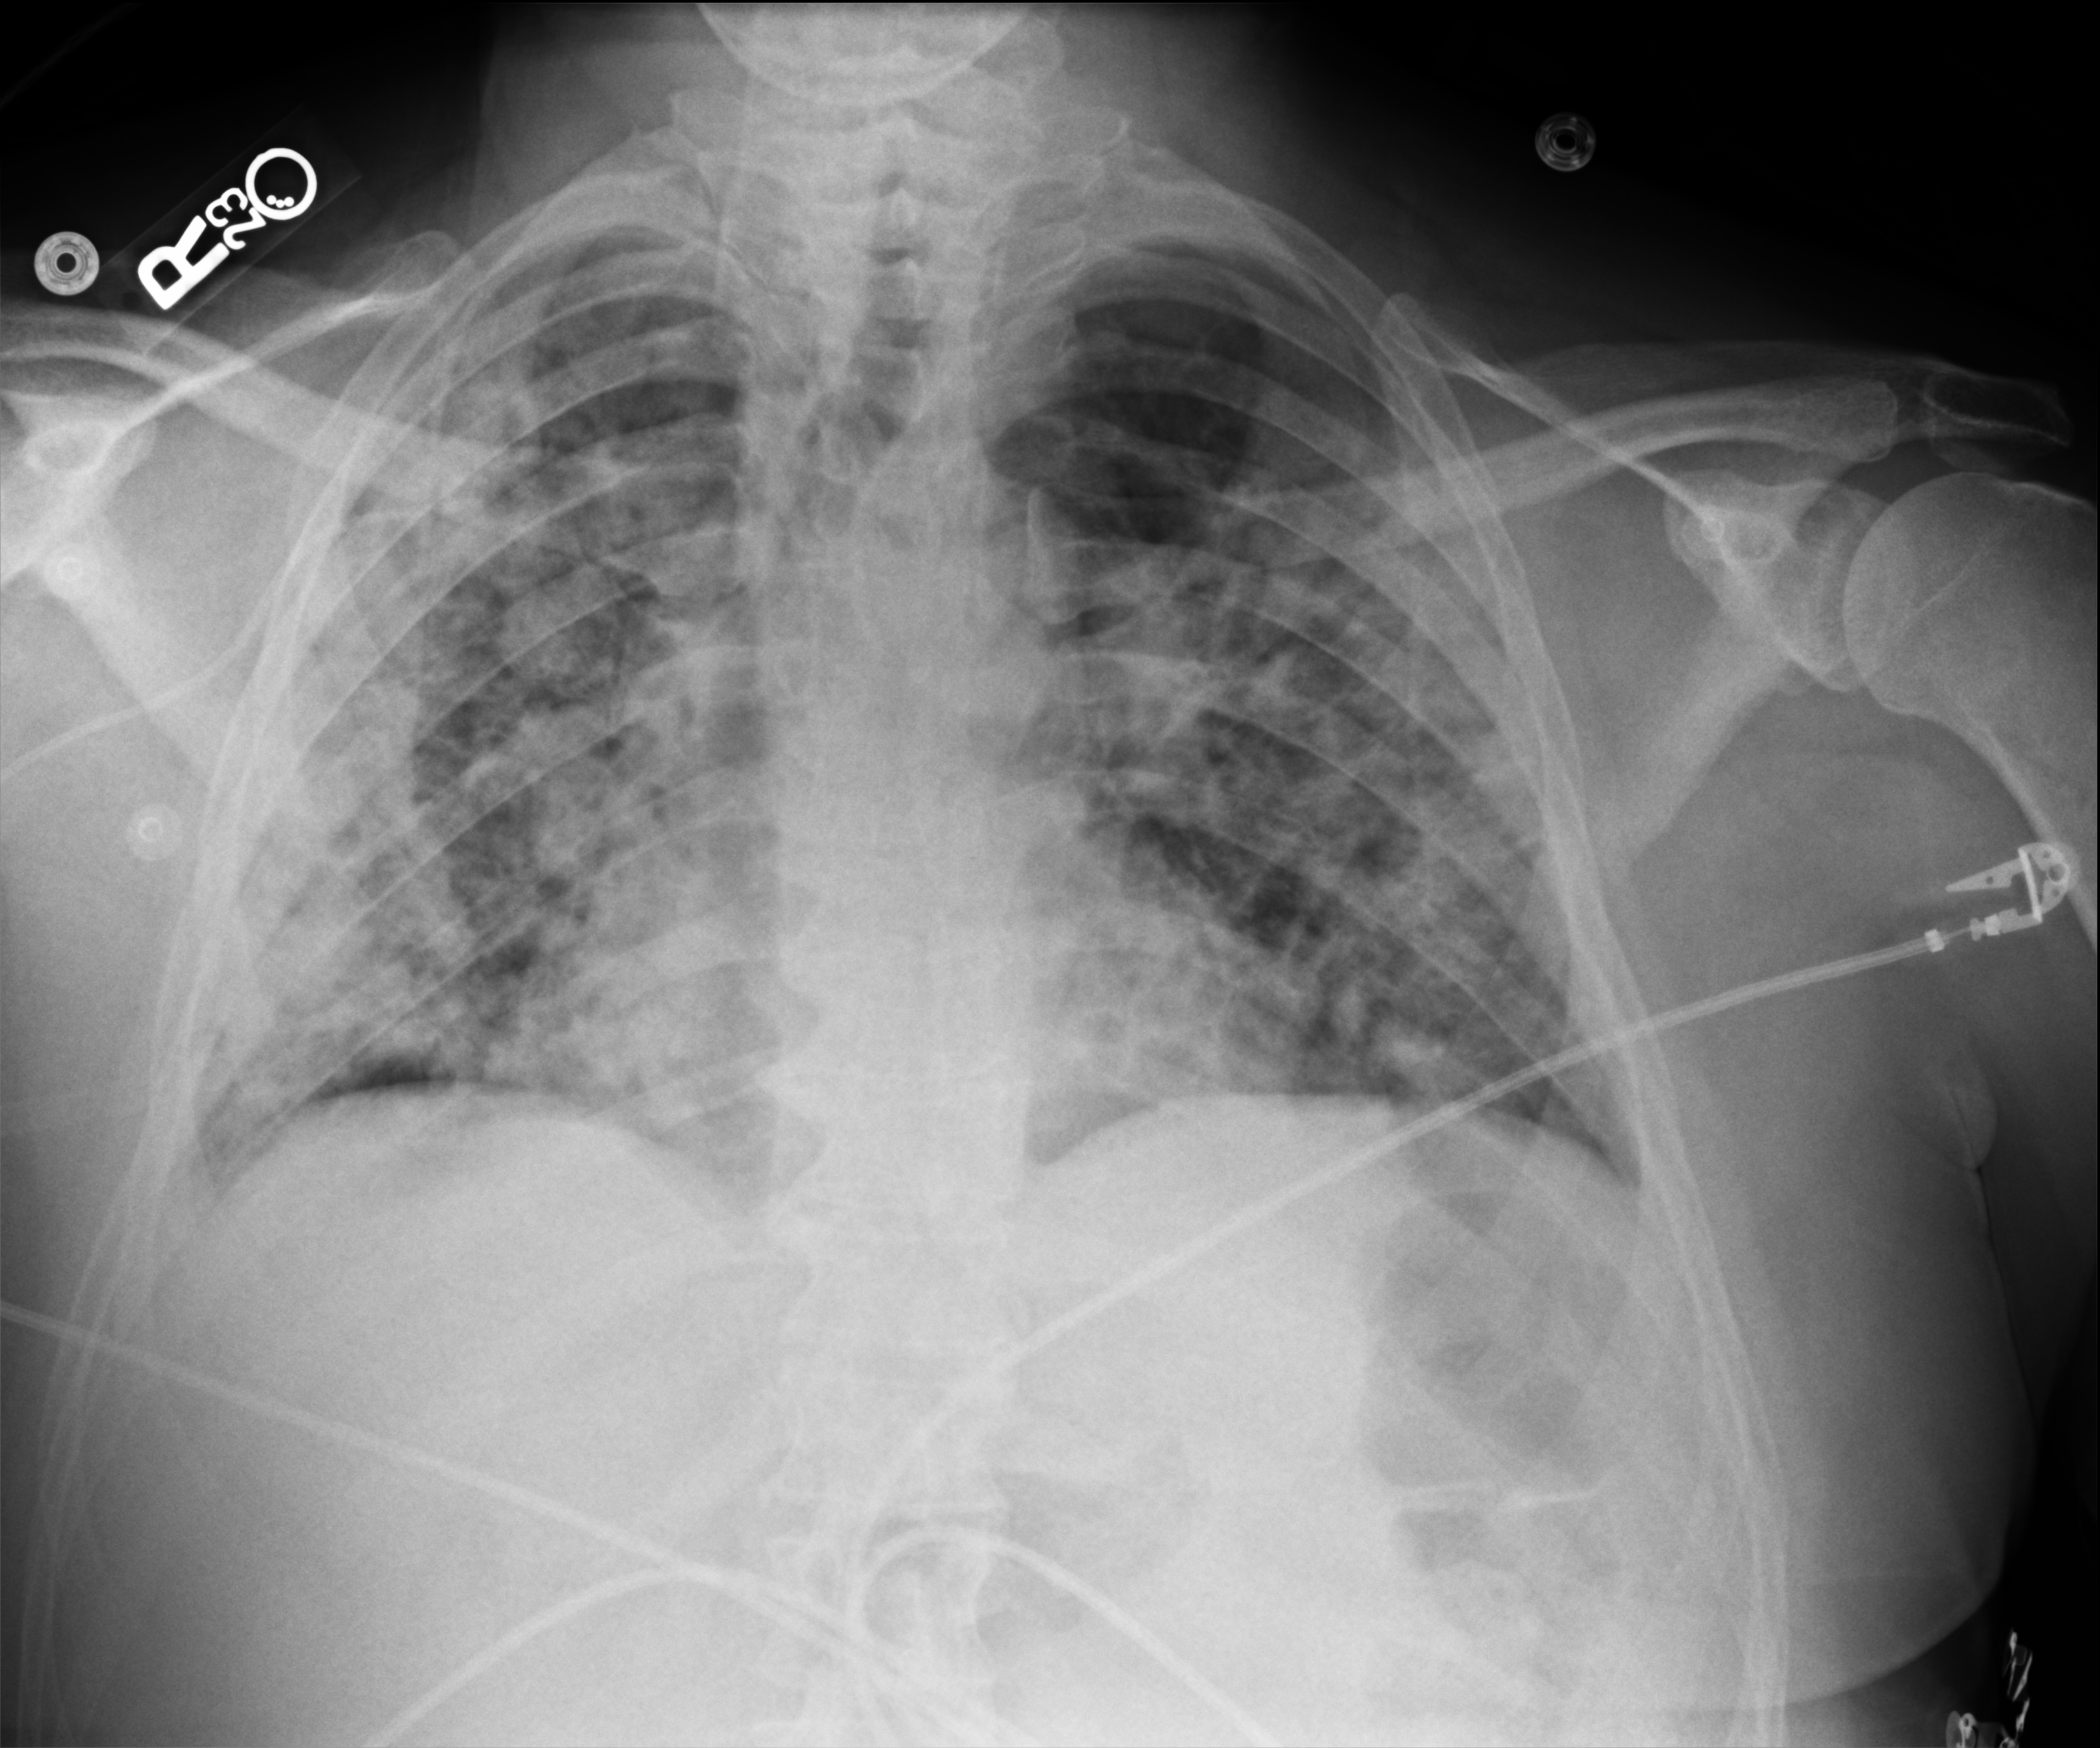
Bedside chest radiograph (computed radiography). Patient hospitalised with COVID-19; male, aged 18–59 years.
From the hospital-stay record, not from the radiograph (when in the stay this image was taken is not recorded): admitted to intensive care during this hospital stay: yes; COPD (admission record): no; smoking status (admission record): never.